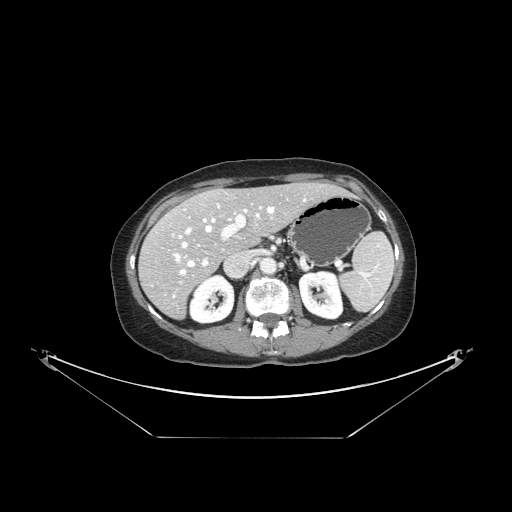
Contrast-enhanced abdominal CT, one axial slice; position 88 of 148 along the scan axis; reconstruction kernel STANDARD; intravenous contrast given; soft-tissue window (W 400 / L 40 HU); 512 × 512 image matrix. Female patient, age 73 years. Case-level facts recorded for this patient, not image findings: diagnosis: colorectal cancer liver metastases, imaged before liver resection.
Annotated regions visible in this slice (expert manual segmentation):
- hepatic veins: box from (x=173, y=200) to (x=305, y=297) px
- liver: (x=140, y=184)–(x=343, y=317)
- planned liver remnant (the part of the liver to remain after resection): (x=168, y=184)–(x=341, y=253)
- portal vein (with intrahepatic branches): (x=172, y=205)–(x=262, y=266)